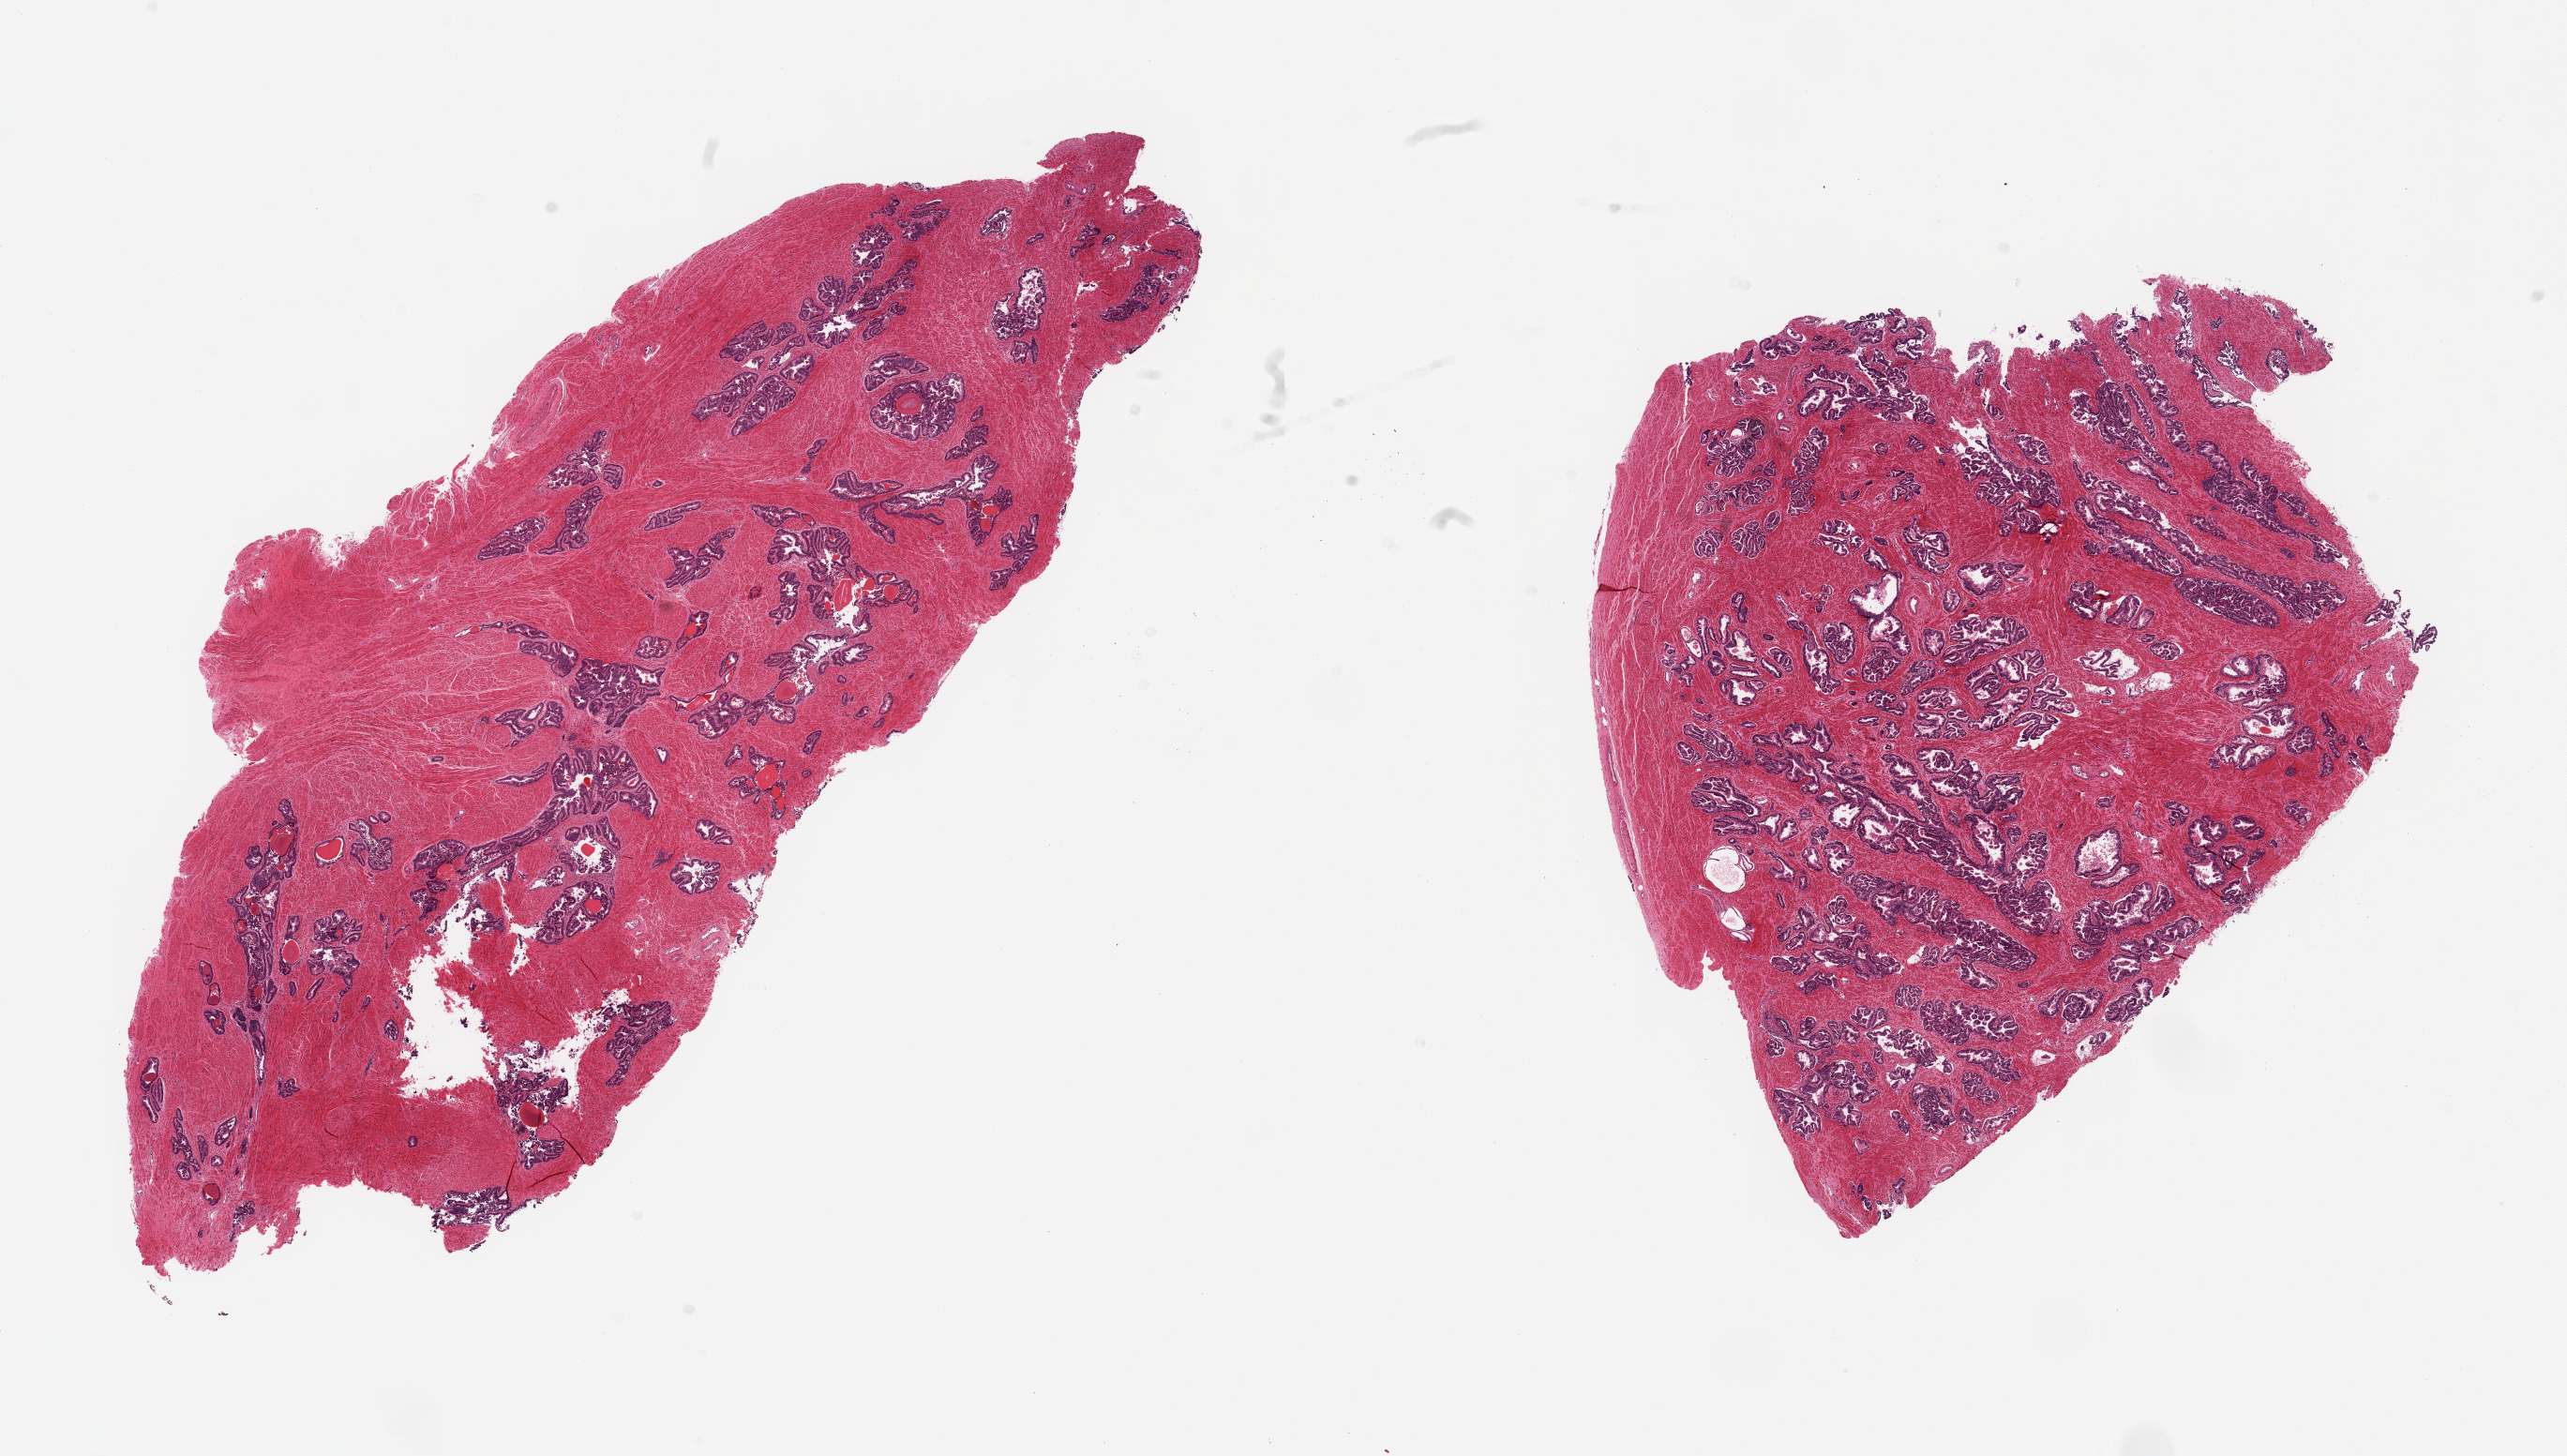
Whole-slide image, hematoxylin and eosin (H&E) stain, brightfield, a low-resolution overview of the entire scanned area, about 21.7 x 12.3 mm; PAXgene-fixed, paraffin-embedded tissue; sampled site (target tissue): prostate; donor tissue sample. Donor: male.
Pathologist's review note for this sample: 2 pieces, hyperplastic glandular pattern.